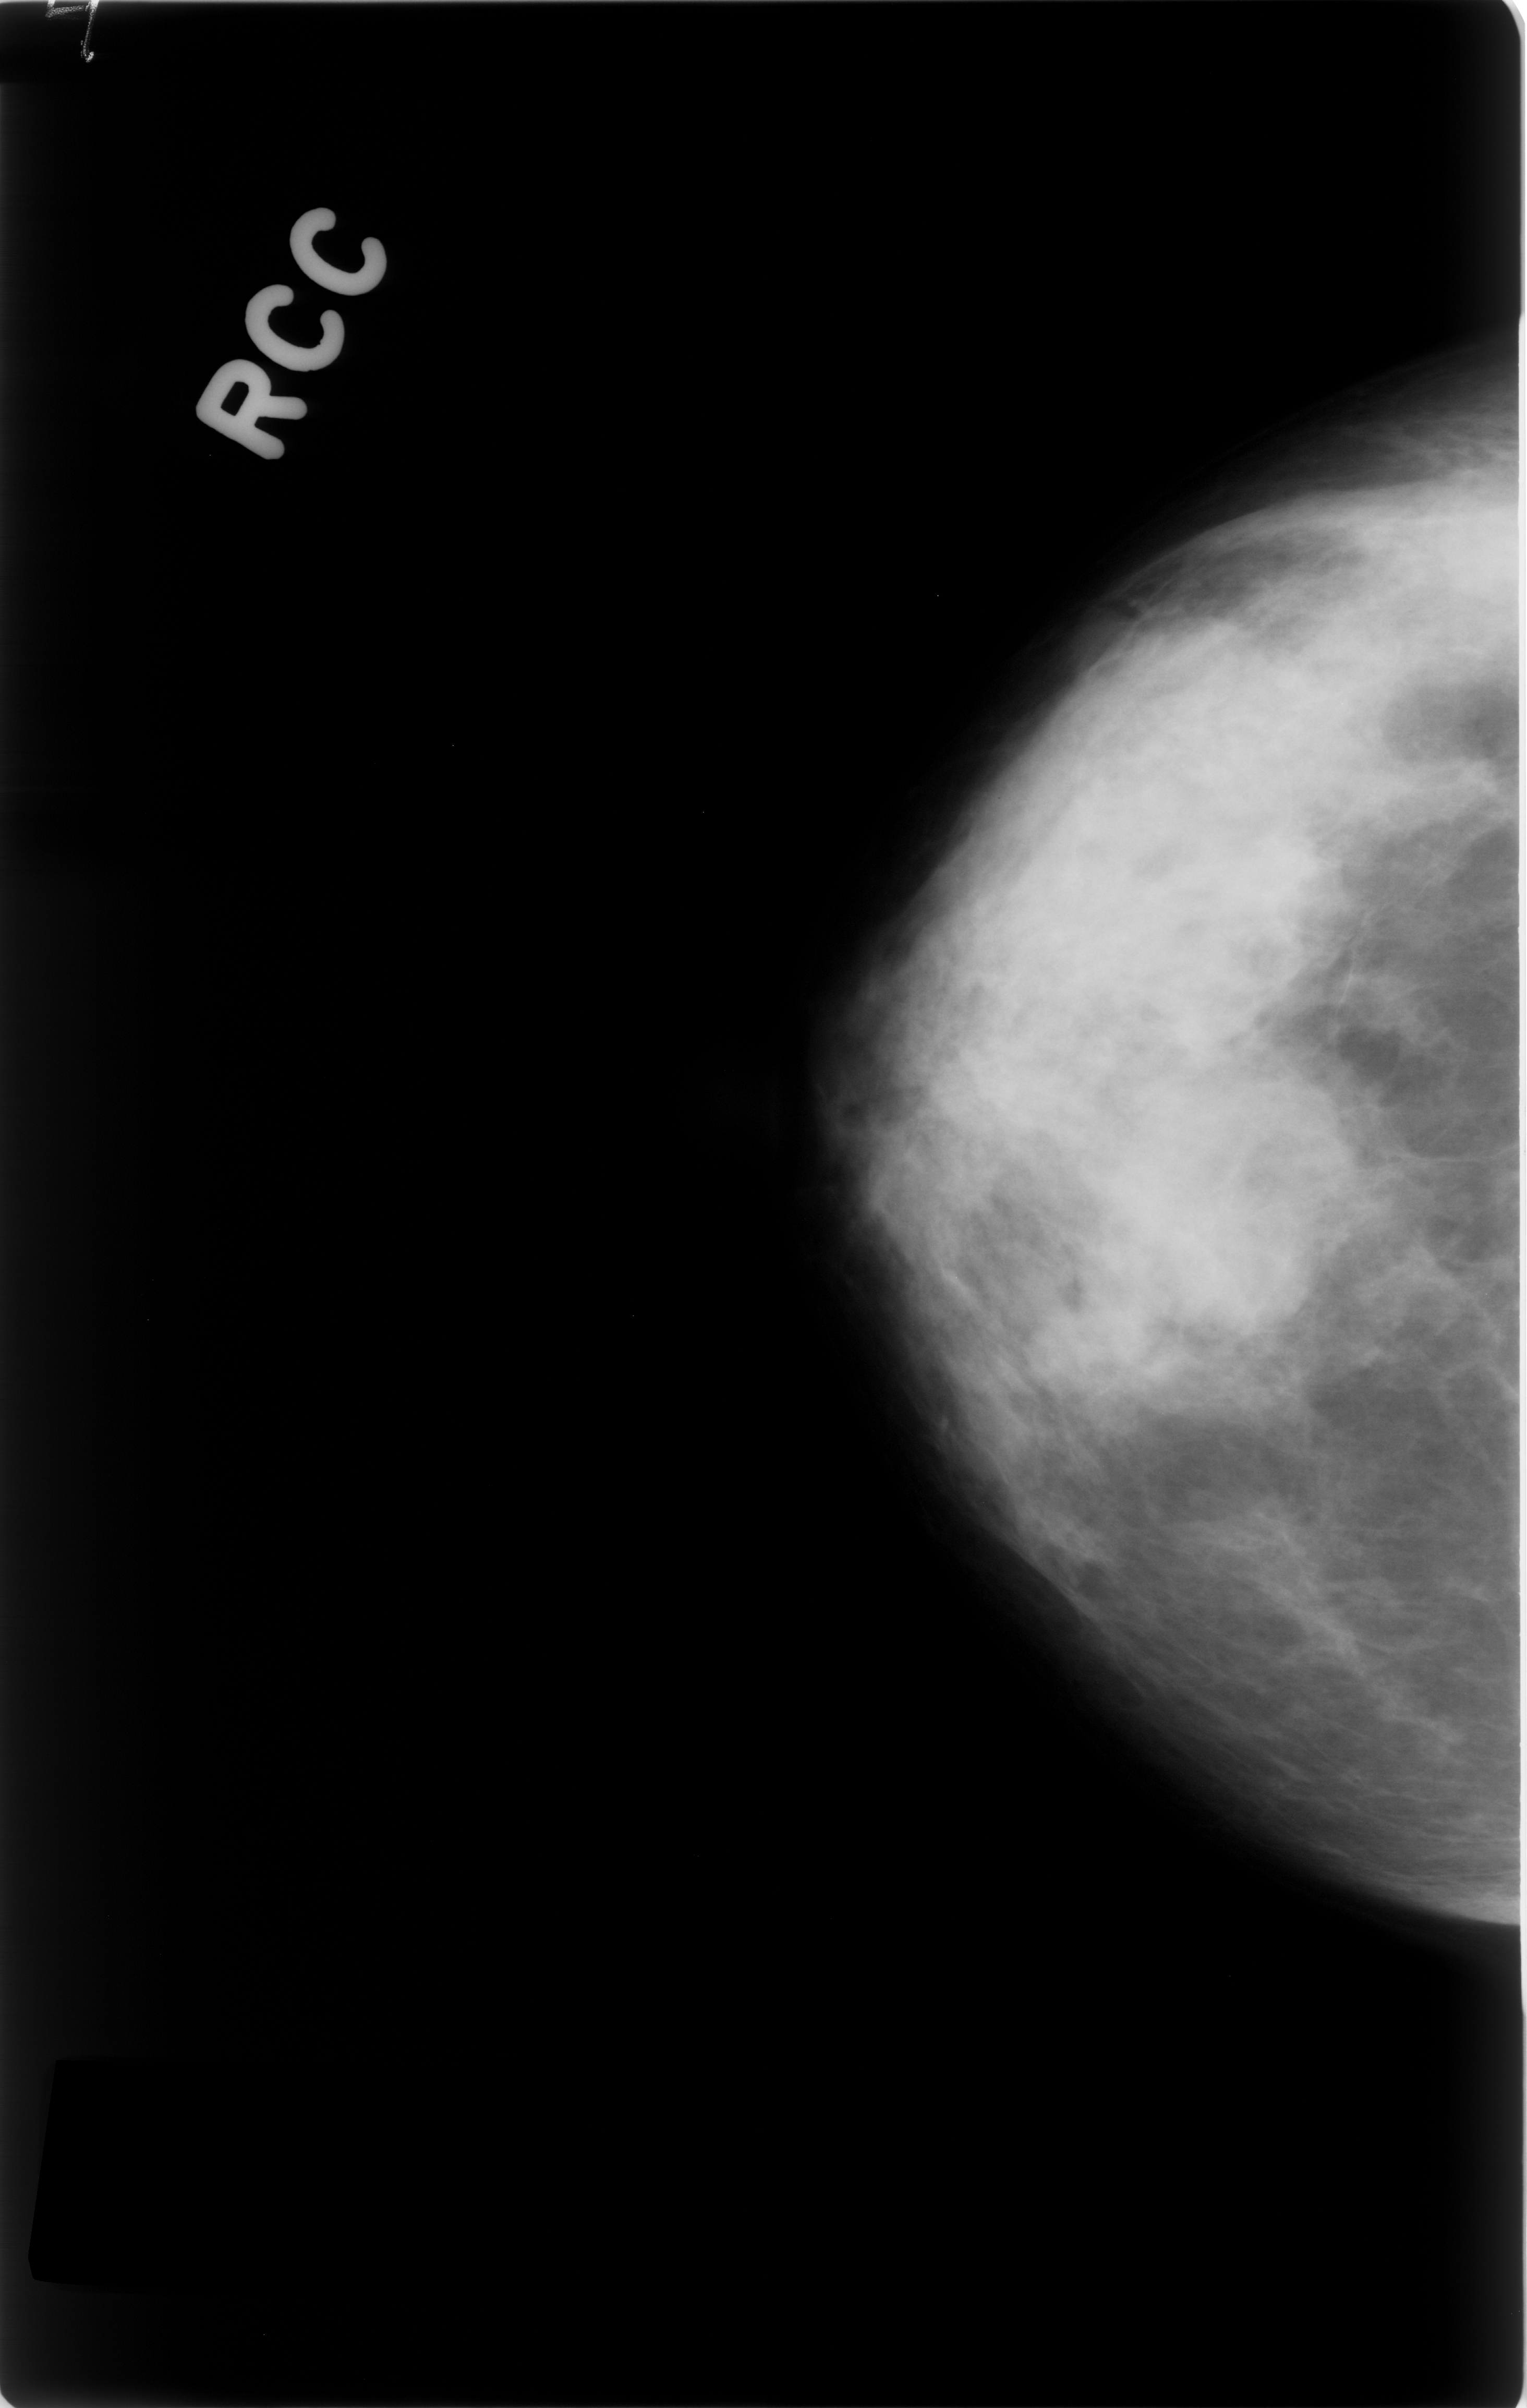
Scanned film-screen mammogram. Right breast. Craniocaudal (CC) view. Breast composition: heterogeneously dense (BI-RADS density category 3 of 4). 1527 × 2408 image matrix.
Expert-marked regions of interest on this film, with their recorded descriptors:
- mass, shape lobulated, margins obscured; BI-RADS assessment category 3; subtlety rating 4 on a 1 (subtle) to 5 (obvious) scale; pathology result (as recorded, not read from the image): benign: box from (x=1123, y=1157) to (x=1329, y=1348) px